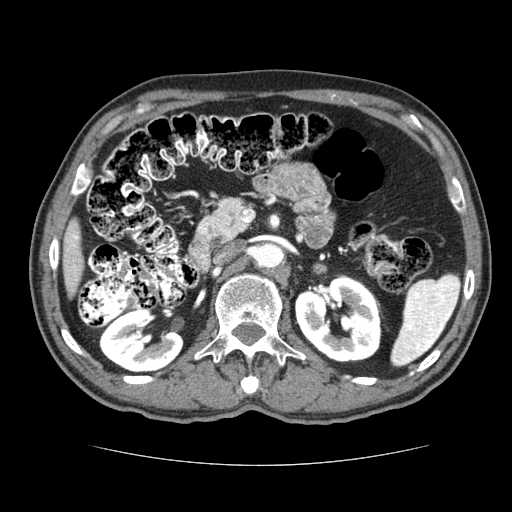
Contrast-enhanced abdominal CT (liver protocol), one axial slice. Position 29 of 79 along the scan axis. 120 kVp. Soft-tissue window (W 400 / L 40 HU). 2.5 mm slice thickness. 512 × 512 image matrix. Case-level facts recorded for this patient, not image findings: diagnosis: hepatocellular carcinoma (patient treated with transarterial chemoembolisation; whether this scan precedes or follows treatment is not stated here); TNM stage (as recorded): Stage-I; Child-Pugh class: A.
Outlined on this slice (semi-automatically segmented with operator editing):
- liver parenchyma outside the tumour (the mass and vessels are separate outlines, so this box may not span the whole liver): box from (x=62, y=218) to (x=82, y=296) px
- liver vessels: (x=72, y=235)–(x=78, y=247)